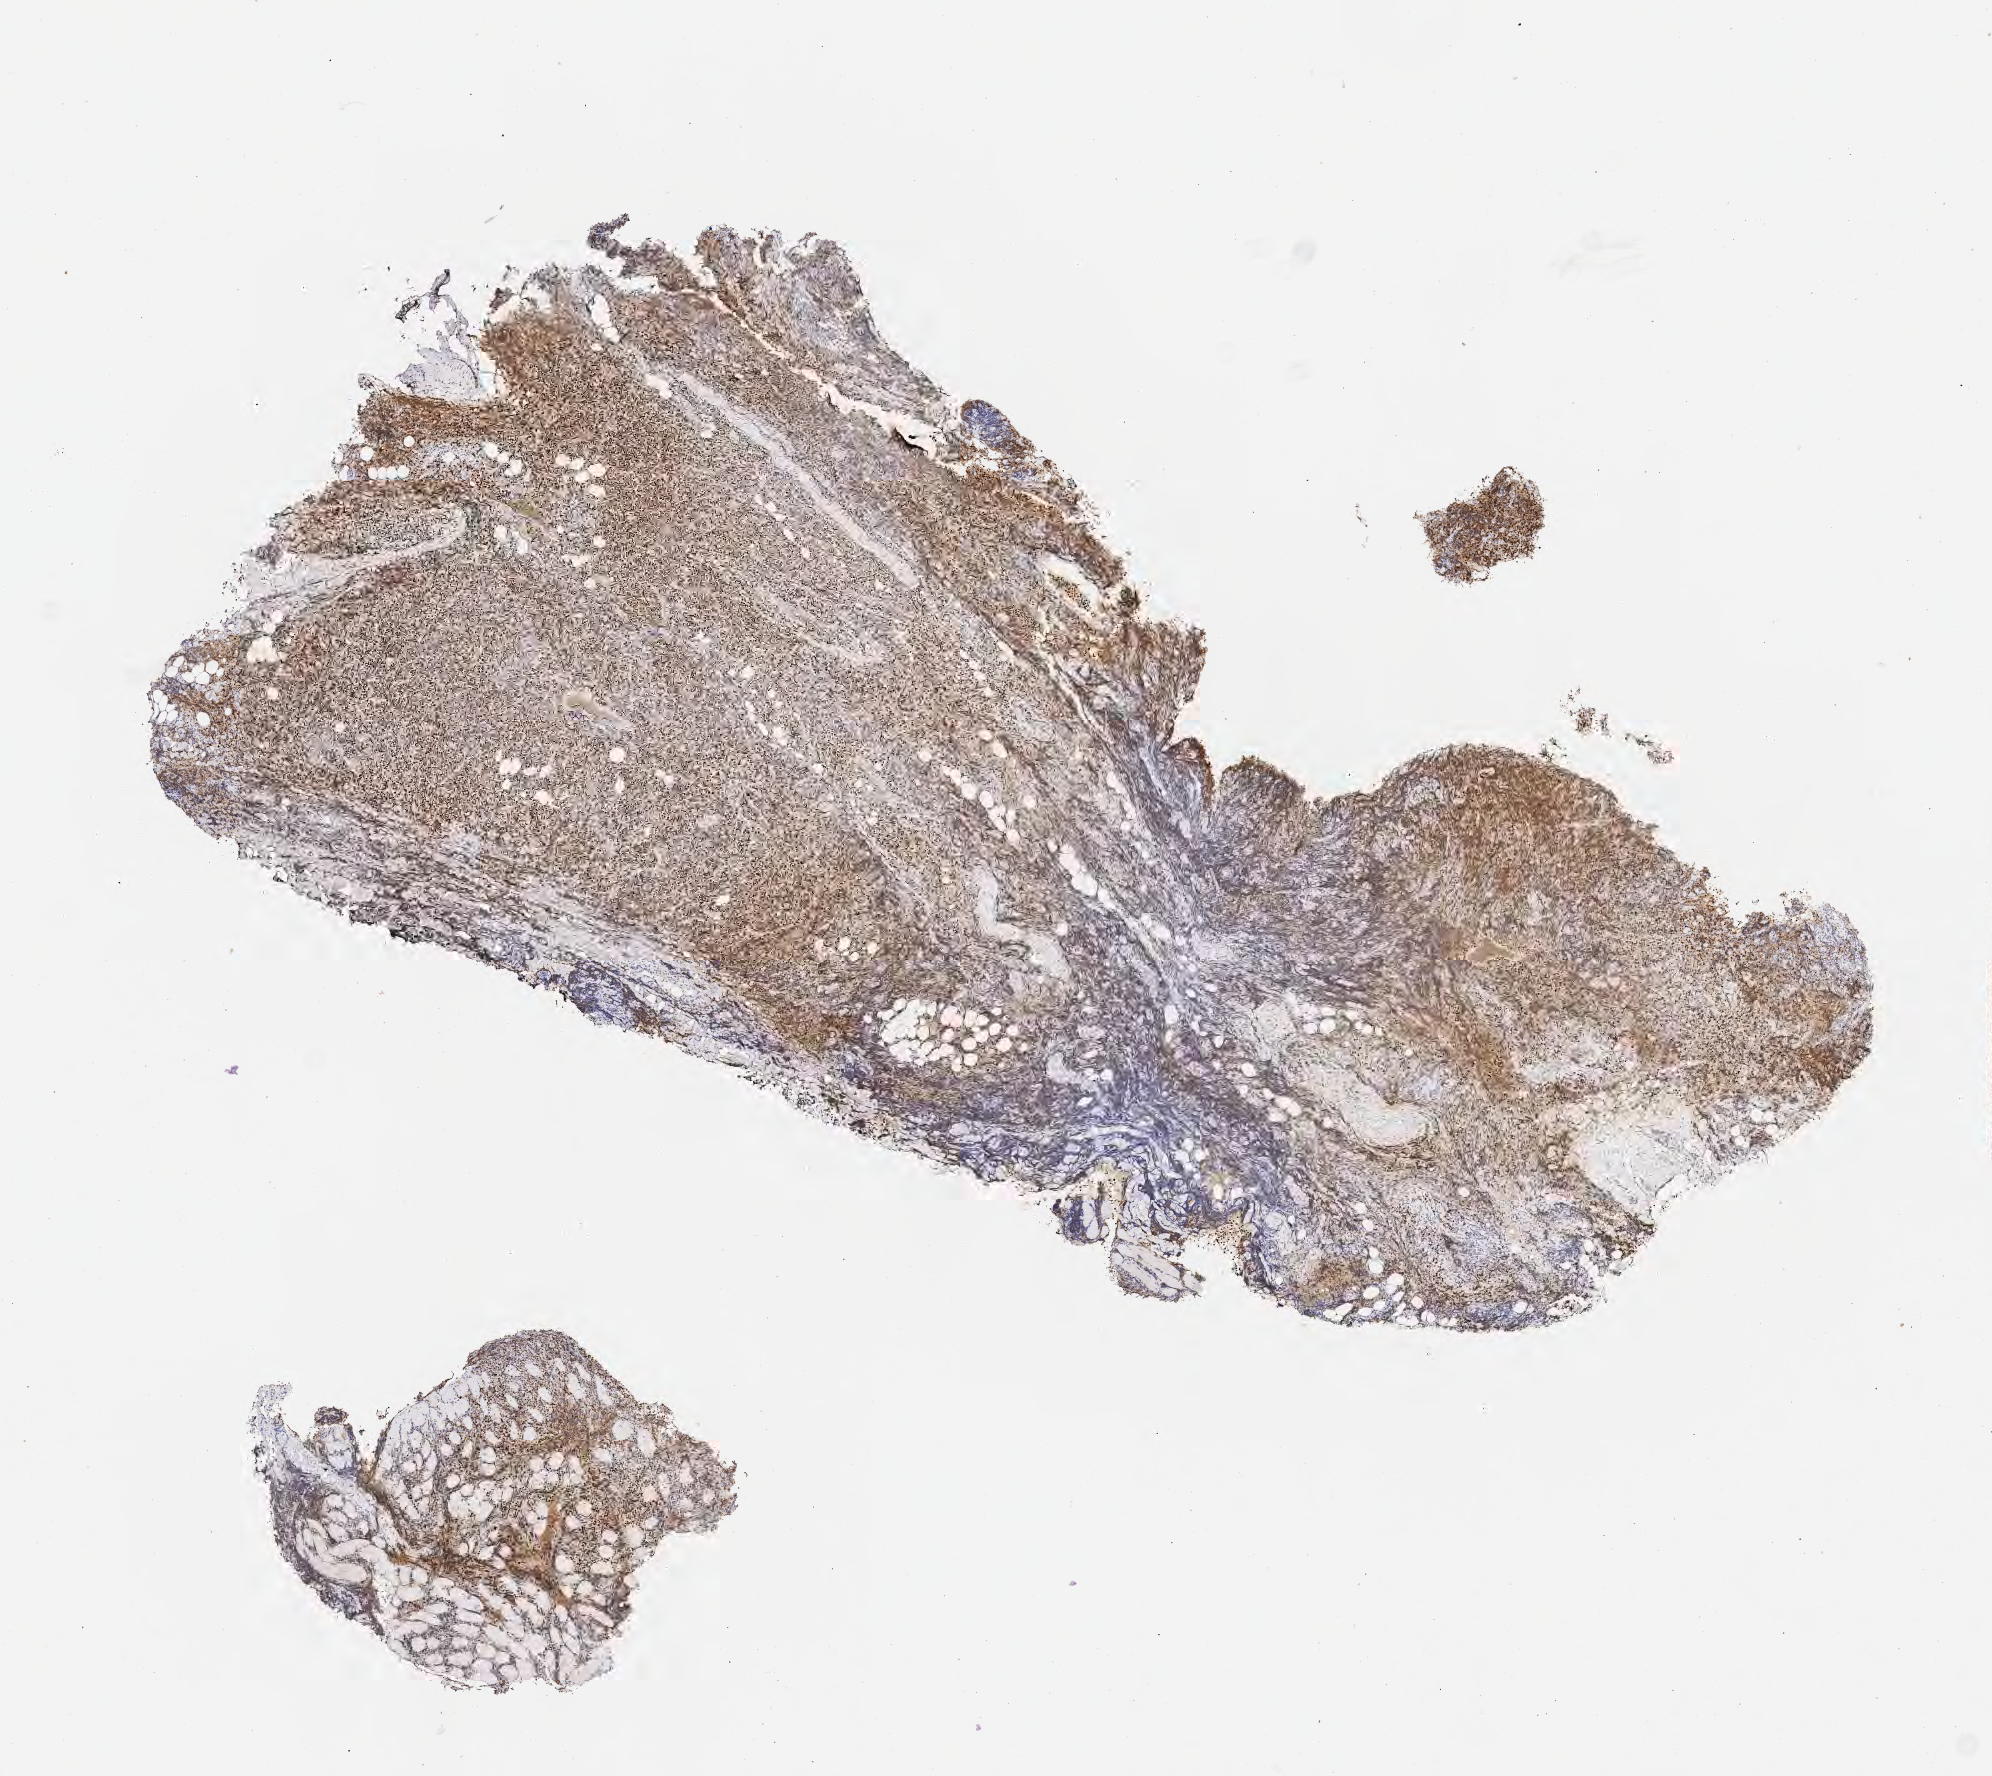
Whole-slide image, immunohistochemical stain for BCL6, a low-resolution overview of the entire scanned area, about 8.0 x 7.2 mm. Tumor tissue. Patient: male, 67 years old.
Diagnosis: Diffuse large B-cell lymphoma, NOS.